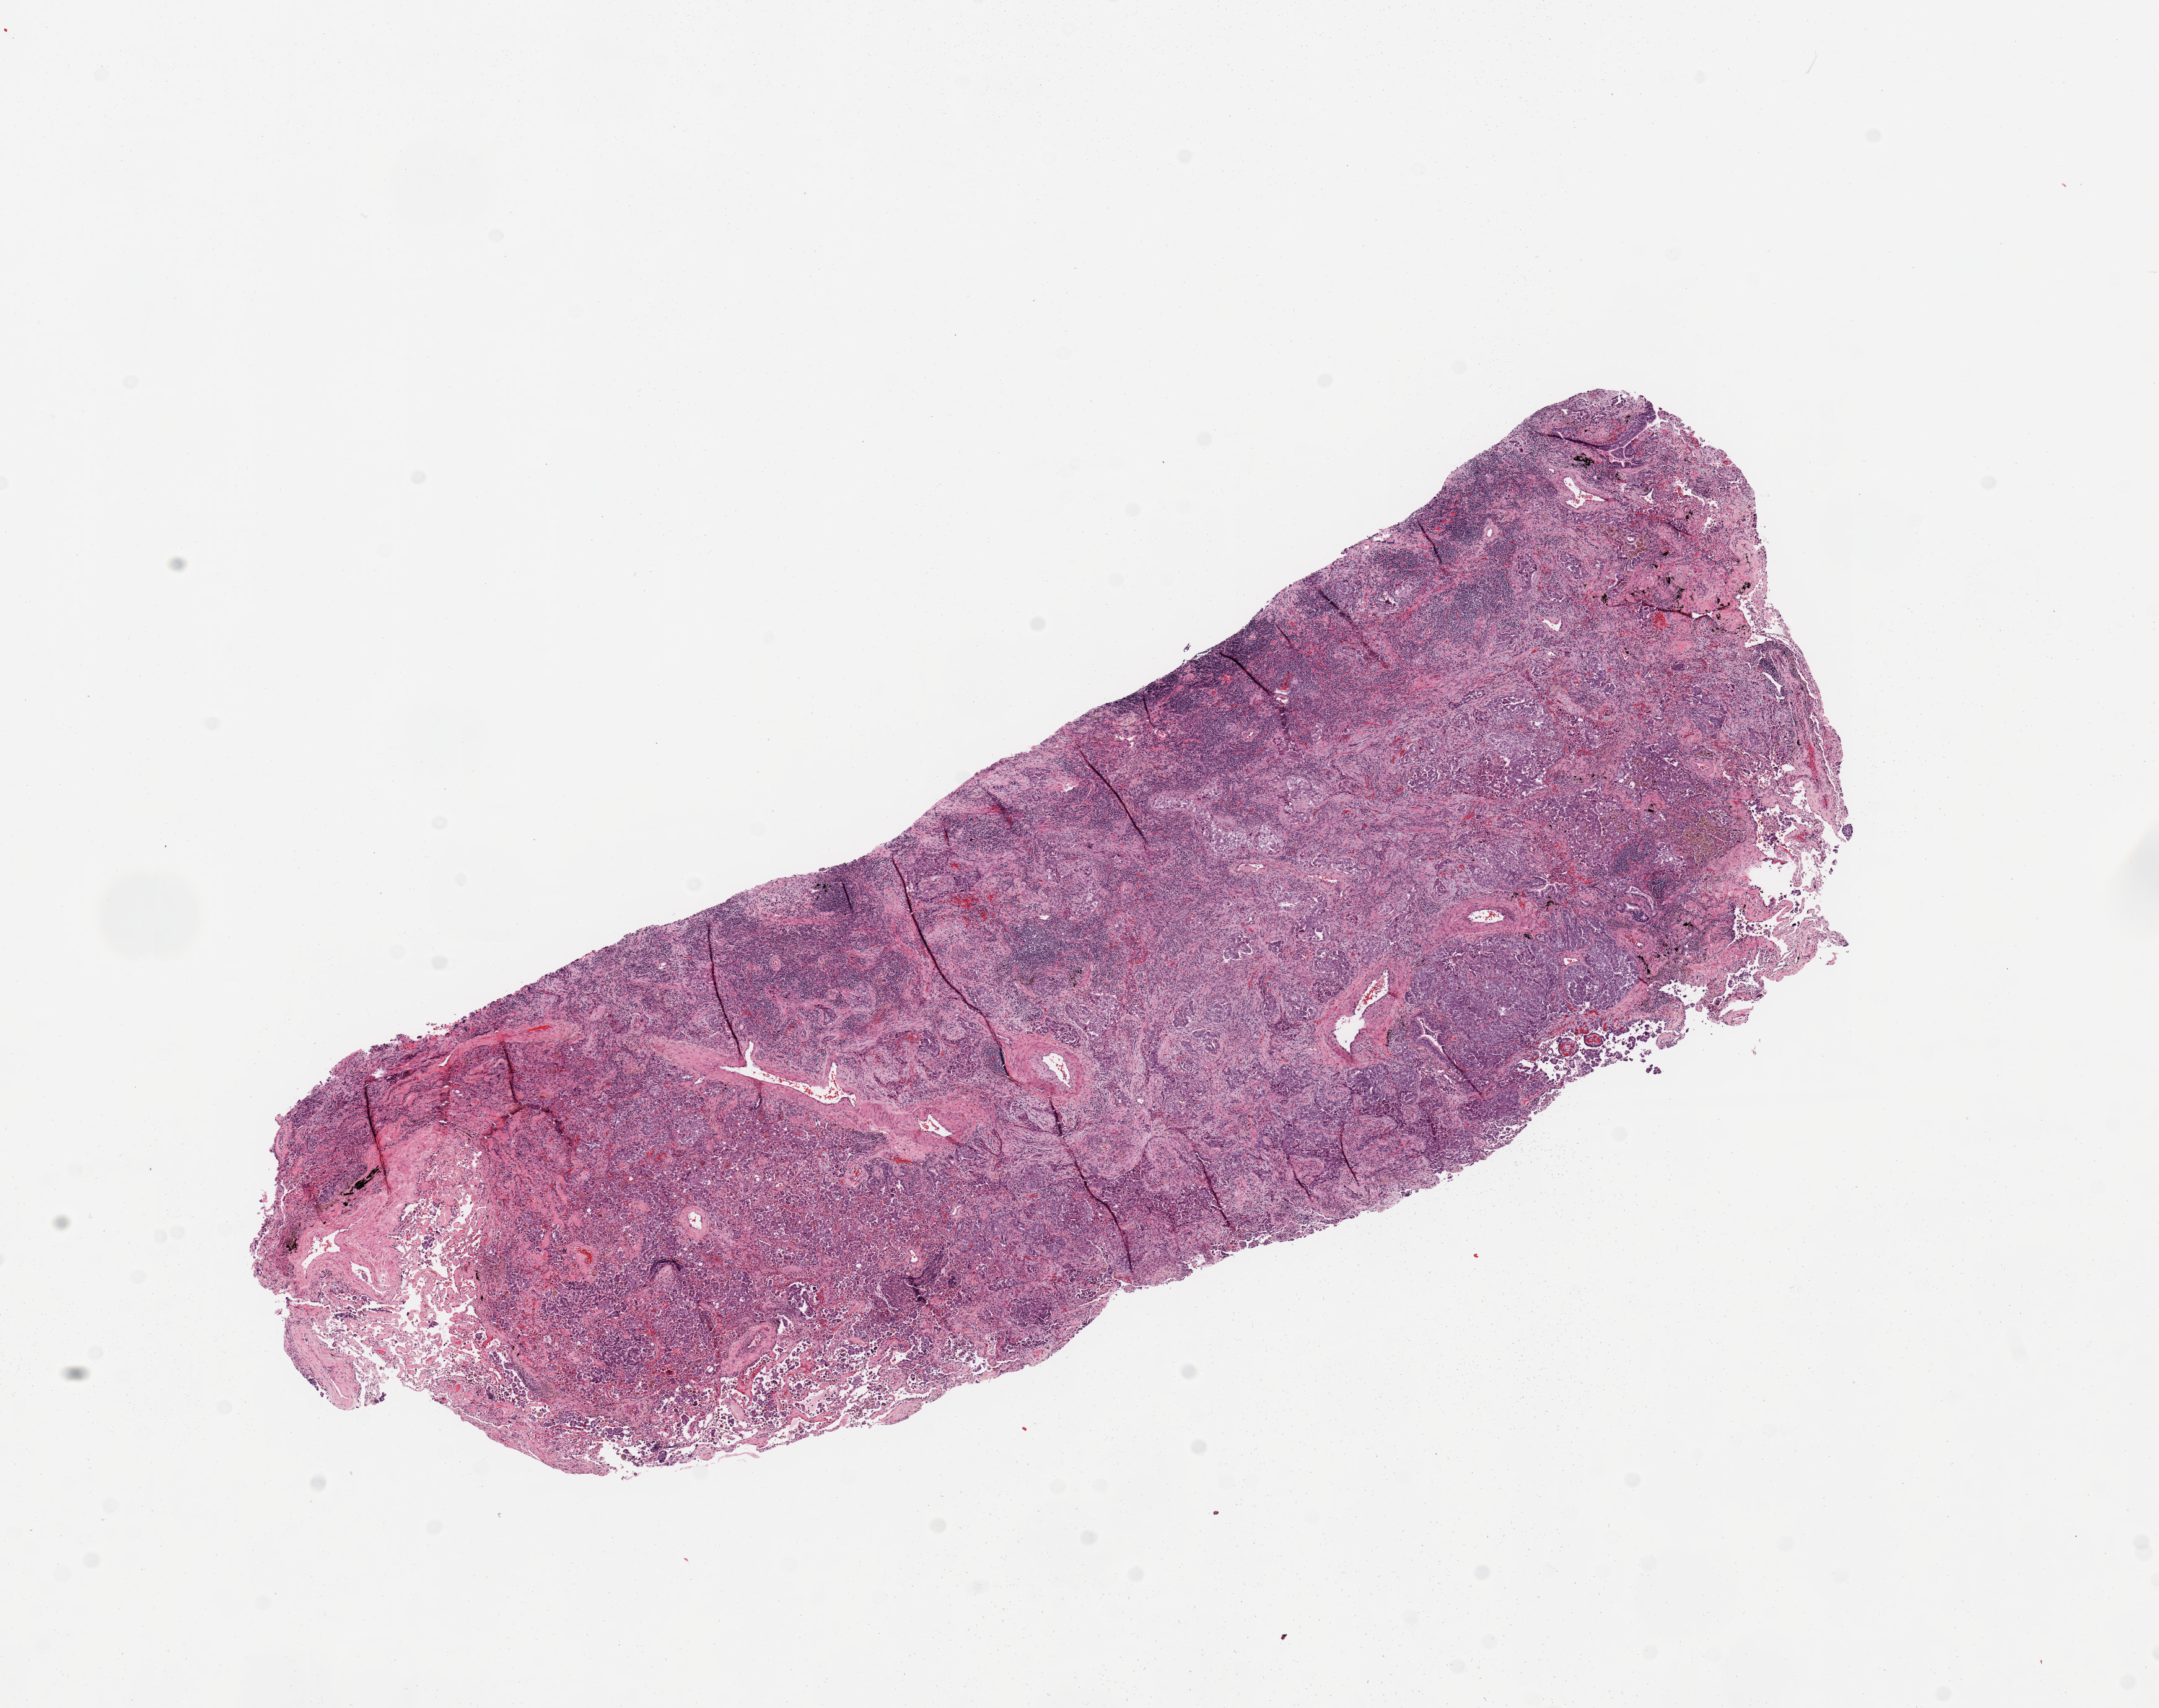
Whole-slide histology image, Hematoxylin and eosin (H&E) stained — a low-resolution overview of the entire scanned area, about 13.8 x 10.9 mm (acquisition: 20x scan); lung, tumour tissue. 62-year-old male patient. Histologic grade: G2 (moderately differentiated).
Primary tumour site (as recorded): left upper lobe. Diagnosis: Adenocarcinoma, NOS. AJCC pathologic stage: IA.